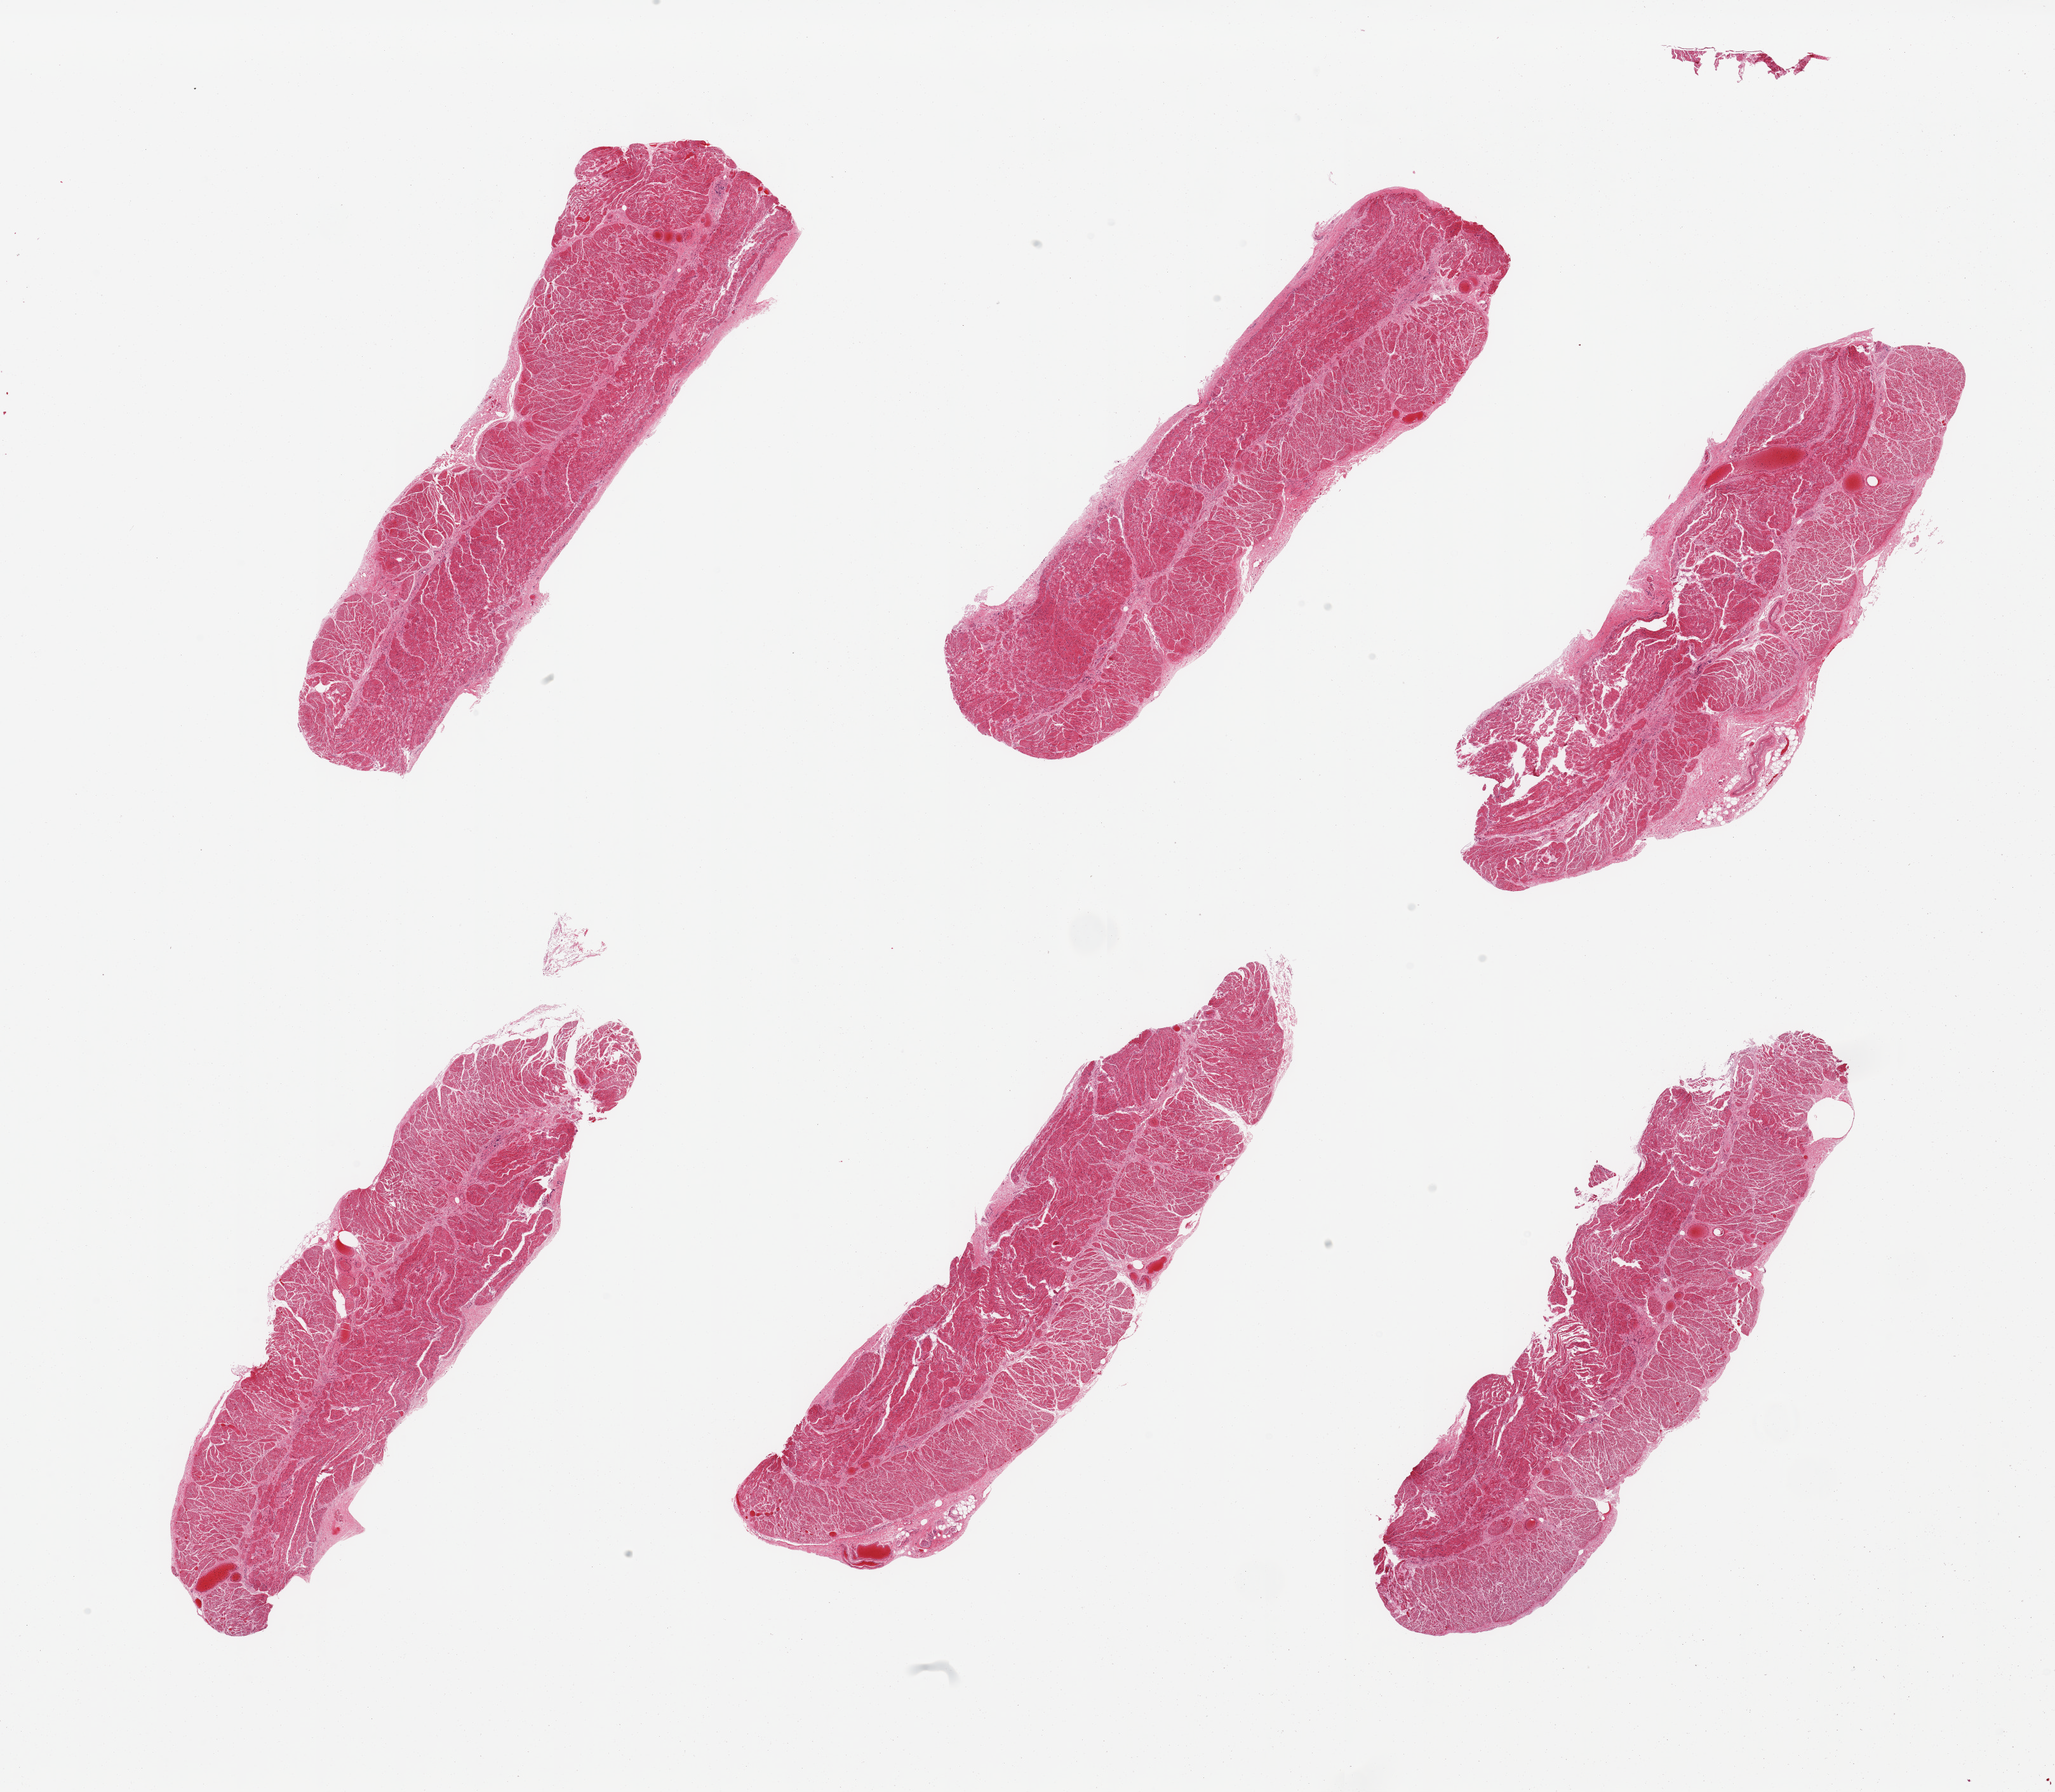
Haematoxylin and eosin whole-slide image — shown as a low-resolution overview of the whole scanned area (about 25.6 x 22.3 mm, slide scanned at 20x). PAXgene-fixed paraffin-embedded (PFPE) section. Section of esophageal muscle (target tissue). Tissue donor sample. Female donor.
Review note (as recorded): 6 pieces, confirmed target muscularis.